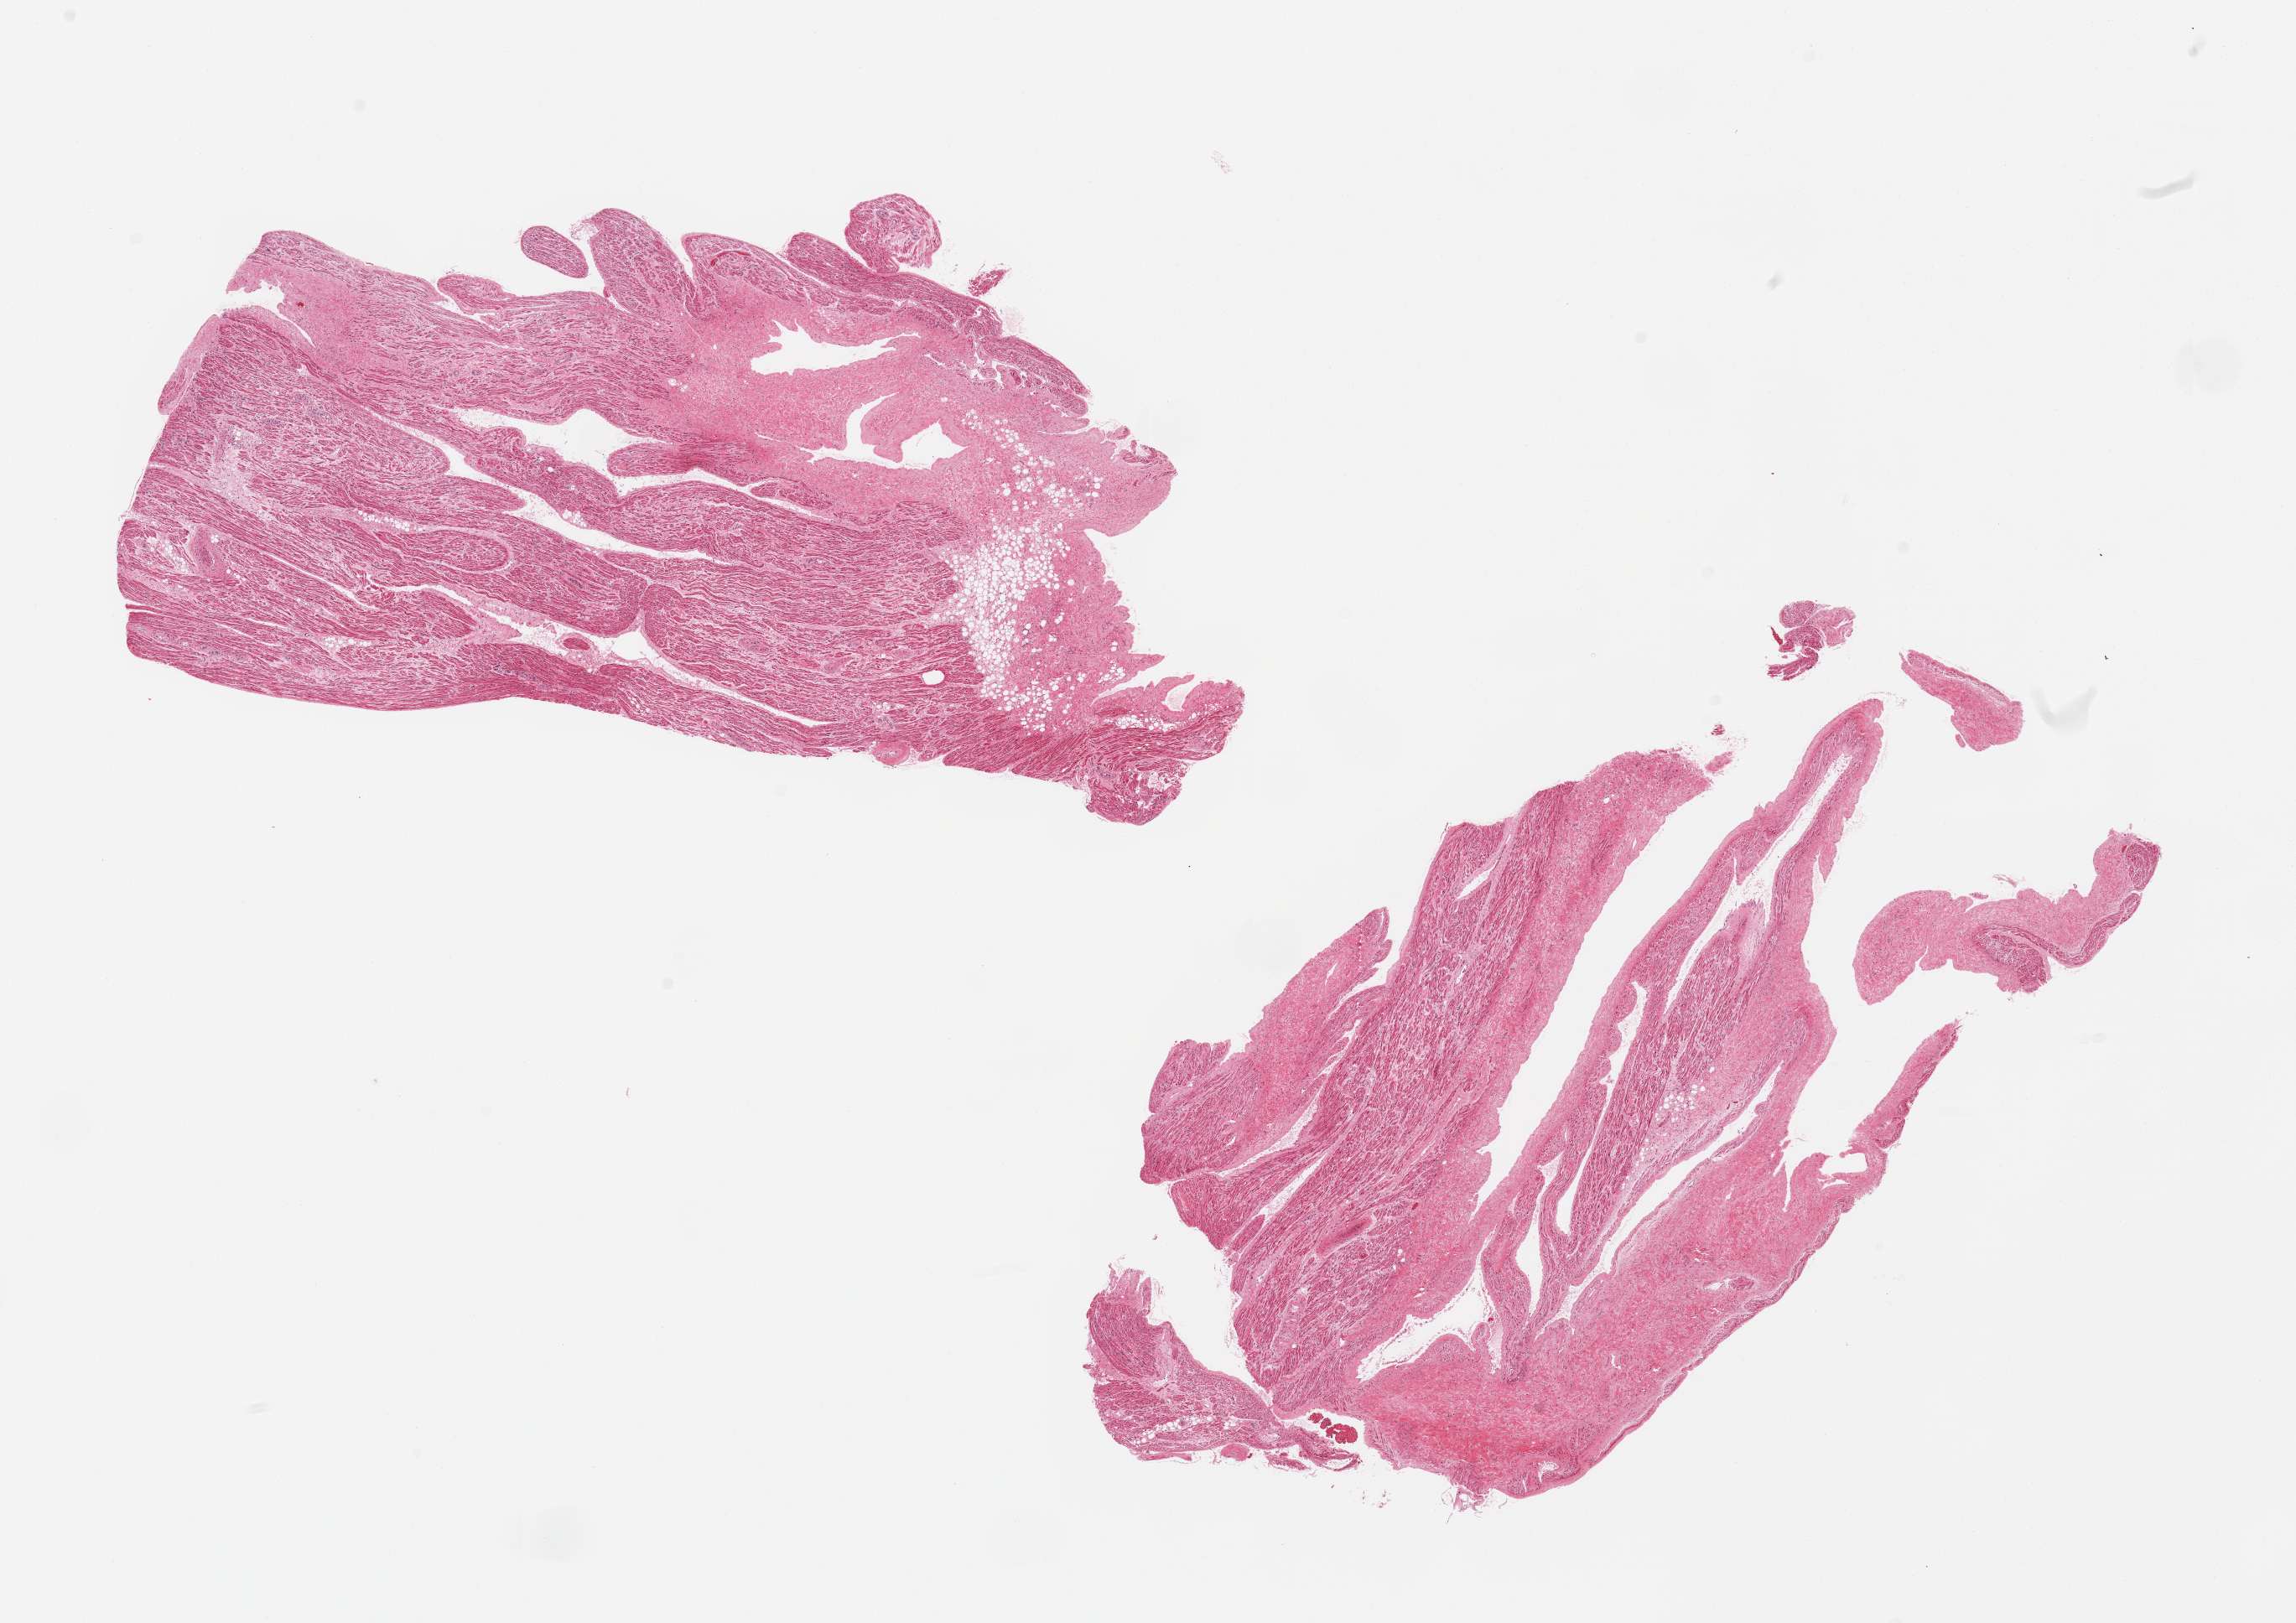
Haematoxylin and eosin whole-slide image, low-resolution overview of the scanned area, about 21.7 x 15.3 mm. PAXgene-fixed paraffin-embedded (PFPE) section. Sampled site (target tissue): auricular appendage. Donor tissue sample. Female donor.
Review note (as recorded): 2 pieces, no abnormalities.